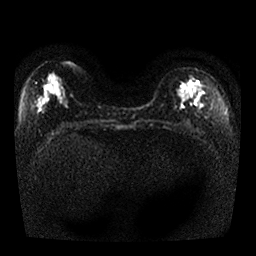
Breast MRI, one axial slice. Slice 12 of 25 in the series (ordered by position). Diffusion-weighted series; image 2 of 4 stored at this slice position (different b-values; order by instance number). 1.5 T. 4 mm slice thickness. 256 × 256 image matrix, field of view 330 × 330 mm. Female patient.
Annotated regions visible in this slice (outlined manually by an expert reader):
- tumour on diffusion-weighted imaging: box from (x=188, y=79) to (x=202, y=88) px